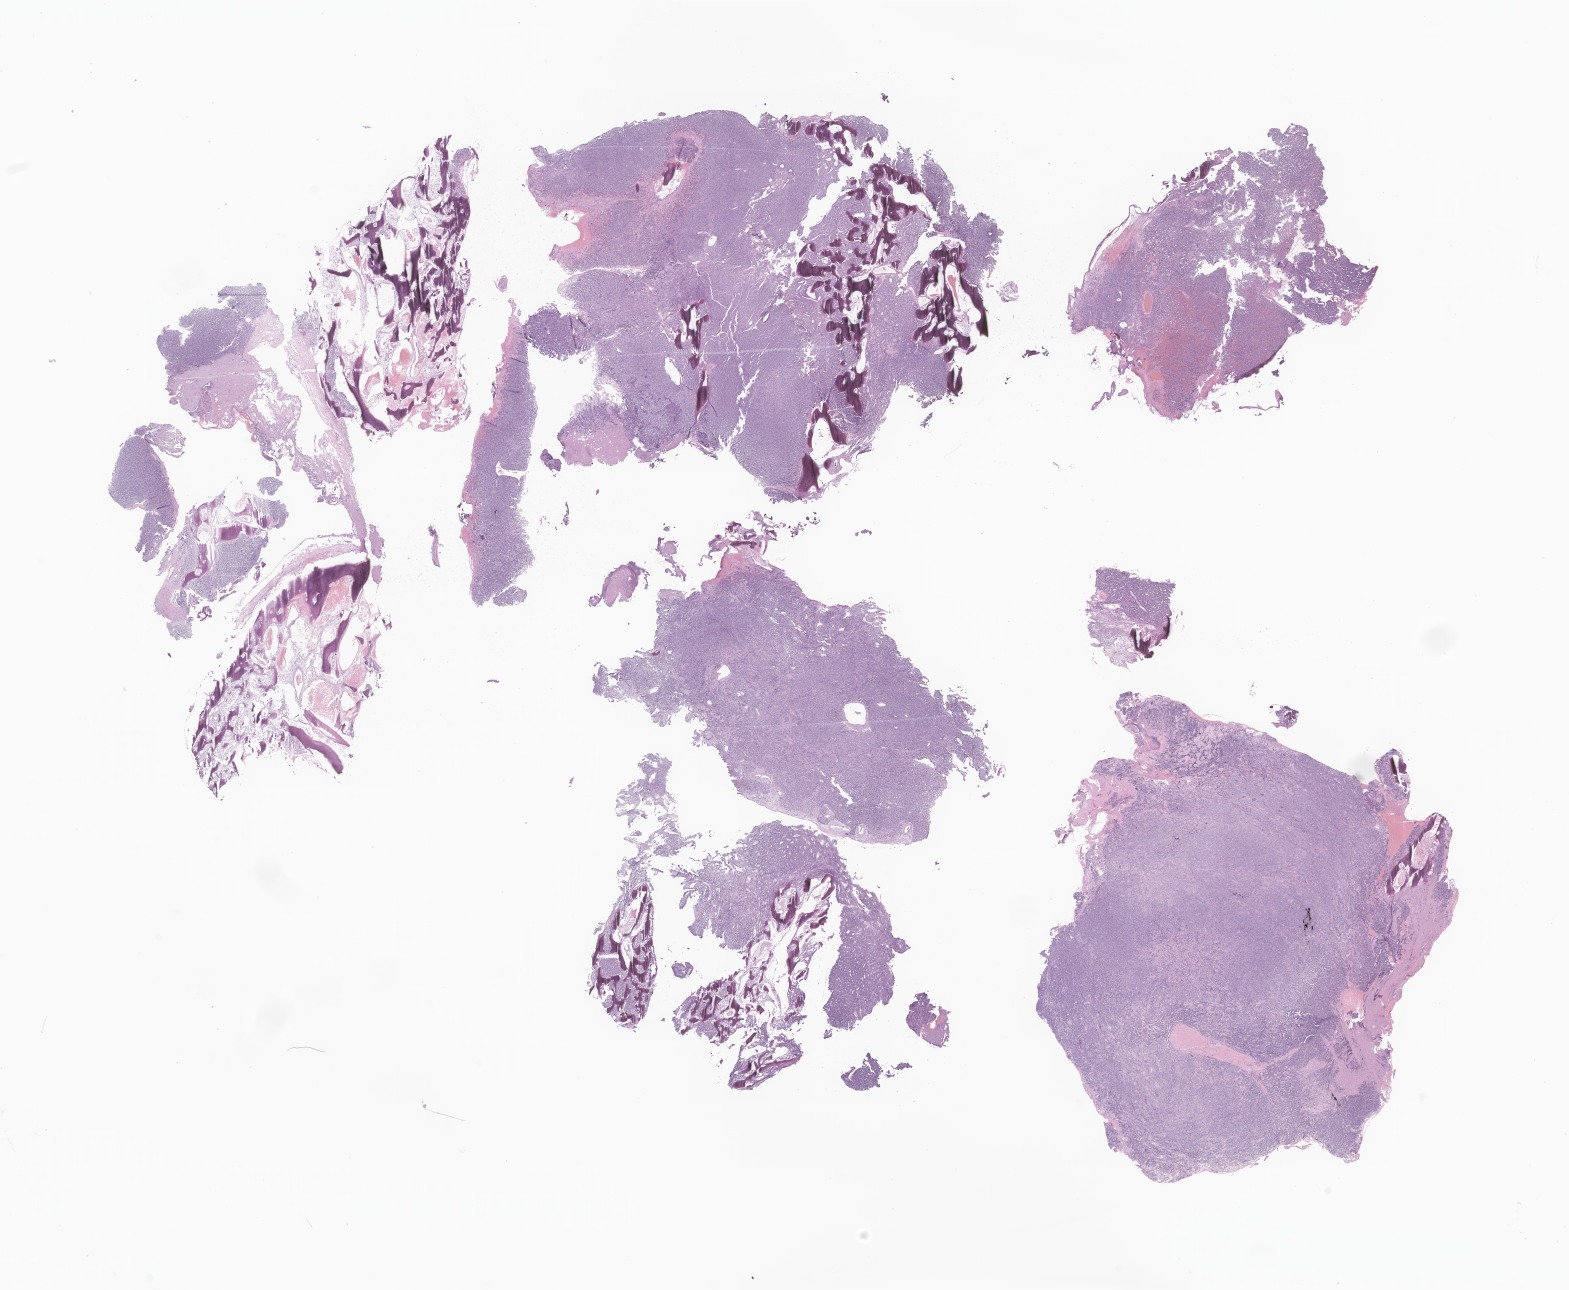
H&E whole-slide image of tumor tissue from the spinal cord, low-resolution overview of the scanned area, about 26.5 x 21.8 mm; formalin-fixed, paraffin-embedded (FFPE) tissue. Female patient, age 131 months (10 years 11 months).
- diagnosis (ICD-O-3 morphology term): Mesenchymal chondrosarcoma